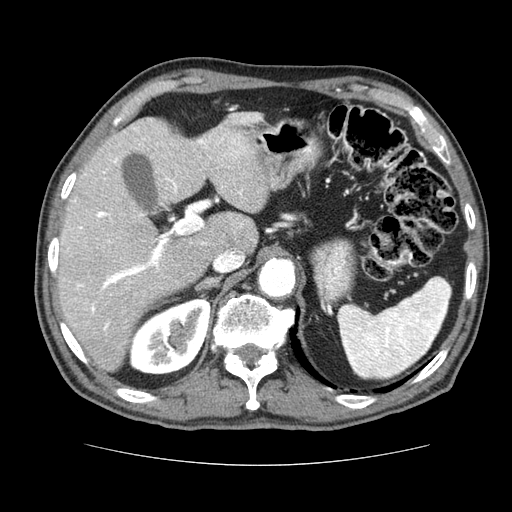
Contrast-enhanced abdominal CT (liver protocol), one axial slice; position 47 of 79 along the scan axis; reconstruction kernel STANDARD; 120 kVp; soft-tissue window (W 400 / L 40 HU); 2.5 mm slice thickness; 512 × 512 image matrix. From the clinical record (not read from this slice): diagnosis: hepatocellular carcinoma (patient treated with transarterial chemoembolisation; whether this scan precedes or follows treatment is not stated here); TNM stage (as recorded): Stage-I; Child-Pugh class: A; tumour nodularity: uninodular.
Annotated regions visible in this slice (semi-automatically segmented with operator editing):
- liver parenchyma outside the tumour (the mass and vessels are separate outlines, so this box may not span the whole liver): bounding box (x1, y1, x2, y2) in pixels: (58, 118, 268, 370)
- liver vessels: (68, 127, 246, 330)